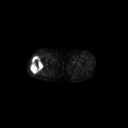
FDG PET of an extremity soft-tissue mass (from a PET/CT study), one axial slice. 3.27 mm slice thickness. 128 × 128 image matrix. Male patient, age 43 years. From the clinical record (not read from this slice): histological type: poorly differentiated synovial sarcoma; grade: high; site of the primary tumour: right buttock.
Outlined on this slice (expert contour drawn on MRI and transferred to this co-registered scan by the dataset authors):
- gross tumour volume including surrounding oedema: box from (x=30, y=57) to (x=43, y=74) px
- gross tumour volume (mass): (x=30, y=57)–(x=43, y=74)